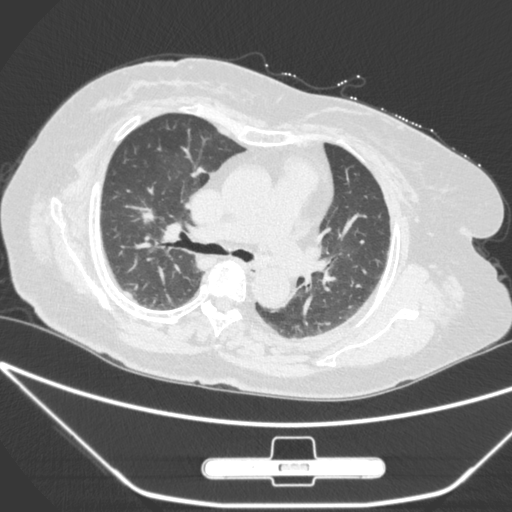
Chest CT, one axial slice. Slice 166 of 245 in the series (ordered by position). Lung window (W 1500 / L -600 HU). 1 mm slice thickness. 512 × 512 image matrix, field of view 365 × 365 mm. Patient: female, 65 years. From the clinical record (not read from this slice): clinical TNM (as recorded): T1c N0 M0.
Outlined on this slice (bounding box drawn by a radiologist):
- lung tumour (recorded histology: adenocarcinoma): box from (x=137, y=204) to (x=161, y=231) px